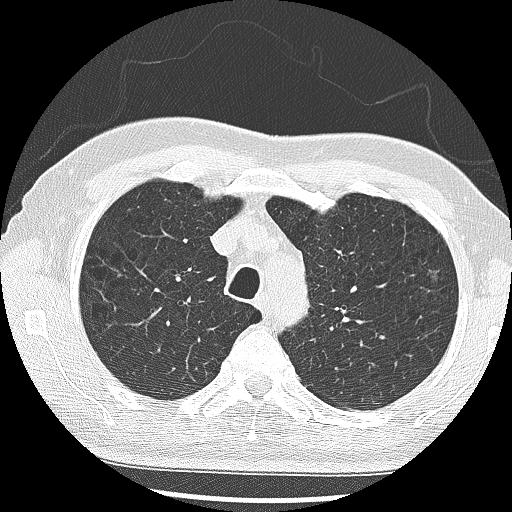
Low-dose screening chest CT, one axial slice. Slice 218 of 285 in the series (ordered by position). 120 kVp. Lung window (W 1500 / L -600 HU). 2.5 mm slice thickness. 512 × 512 image matrix, field of view 340 × 340 mm.
Structures marked on this image (outlined manually by an expert reader):
- lesion 1 (tumor, upper lobe of left lung): bounding box (x1, y1, x2, y2) in pixels: (431, 273, 443, 284)